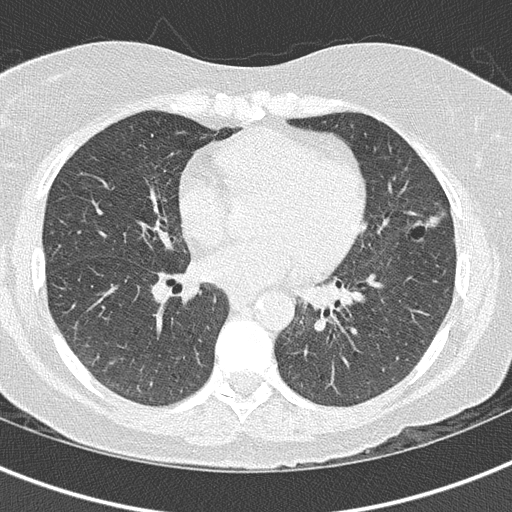
Low-dose screening chest CT, axial slice, third annual screen, lung window (W 1500 / L -600 HU), lung (sharp) reconstruction kernel (B50f), 512 × 512 image matrix. Female participant, aged 63 years at enrolment.
- Expert-annotated lung lesion, bounding box (x1, y1, x2, y2) in pixels: (392, 196, 460, 251).
- The screening reader recorded 5 non-calcified nodules or masses ≥4 mm on this exam (lingula, left lower lobe, right upper lobe, right upper lobe, right upper lobe); which of them this box marks is not recorded.
- Lung cancer was diagnosed 35 days after this screen: bronchiolo-alveolar adenocarcinoma, NOS, lingula, stage IA (AJCC 6th edition), 14 mm at pathology.